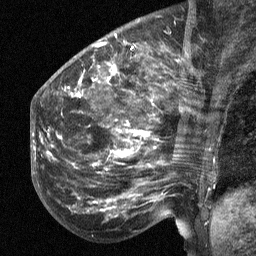
Breast MRI (dynamic contrast-enhanced), one sagittal slice. Position 21 of 64 along the scan axis. Dynamic contrast-enhanced study with each time point stored as its own series, time point 2 of 3 at this slice position (early post-contrast, ordered by acquisition time). 1.5 T. TE 4.8 ms, TR 27 ms. 2.3 mm slice thickness. 256 × 256 image matrix, field of view 200 × 200 mm. Patient: female, 50 years. Case-level facts recorded for this patient, not image findings: setting: breast cancer imaged before/during neoadjuvant chemotherapy; receptor status: HER2-positive.
Annotated regions visible in this slice (semi-automatic segmentation, software-assisted and operator-edited):
- analysis volume of interest (the breast-tissue region the enhancement analysis was run in; not a lesion): box from (x=53, y=64) to (x=211, y=218) px
- tumour enhancement mask (voxels above the 90 % enhancement threshold inside the analysis volume of interest): (x=68, y=65)–(x=157, y=203)